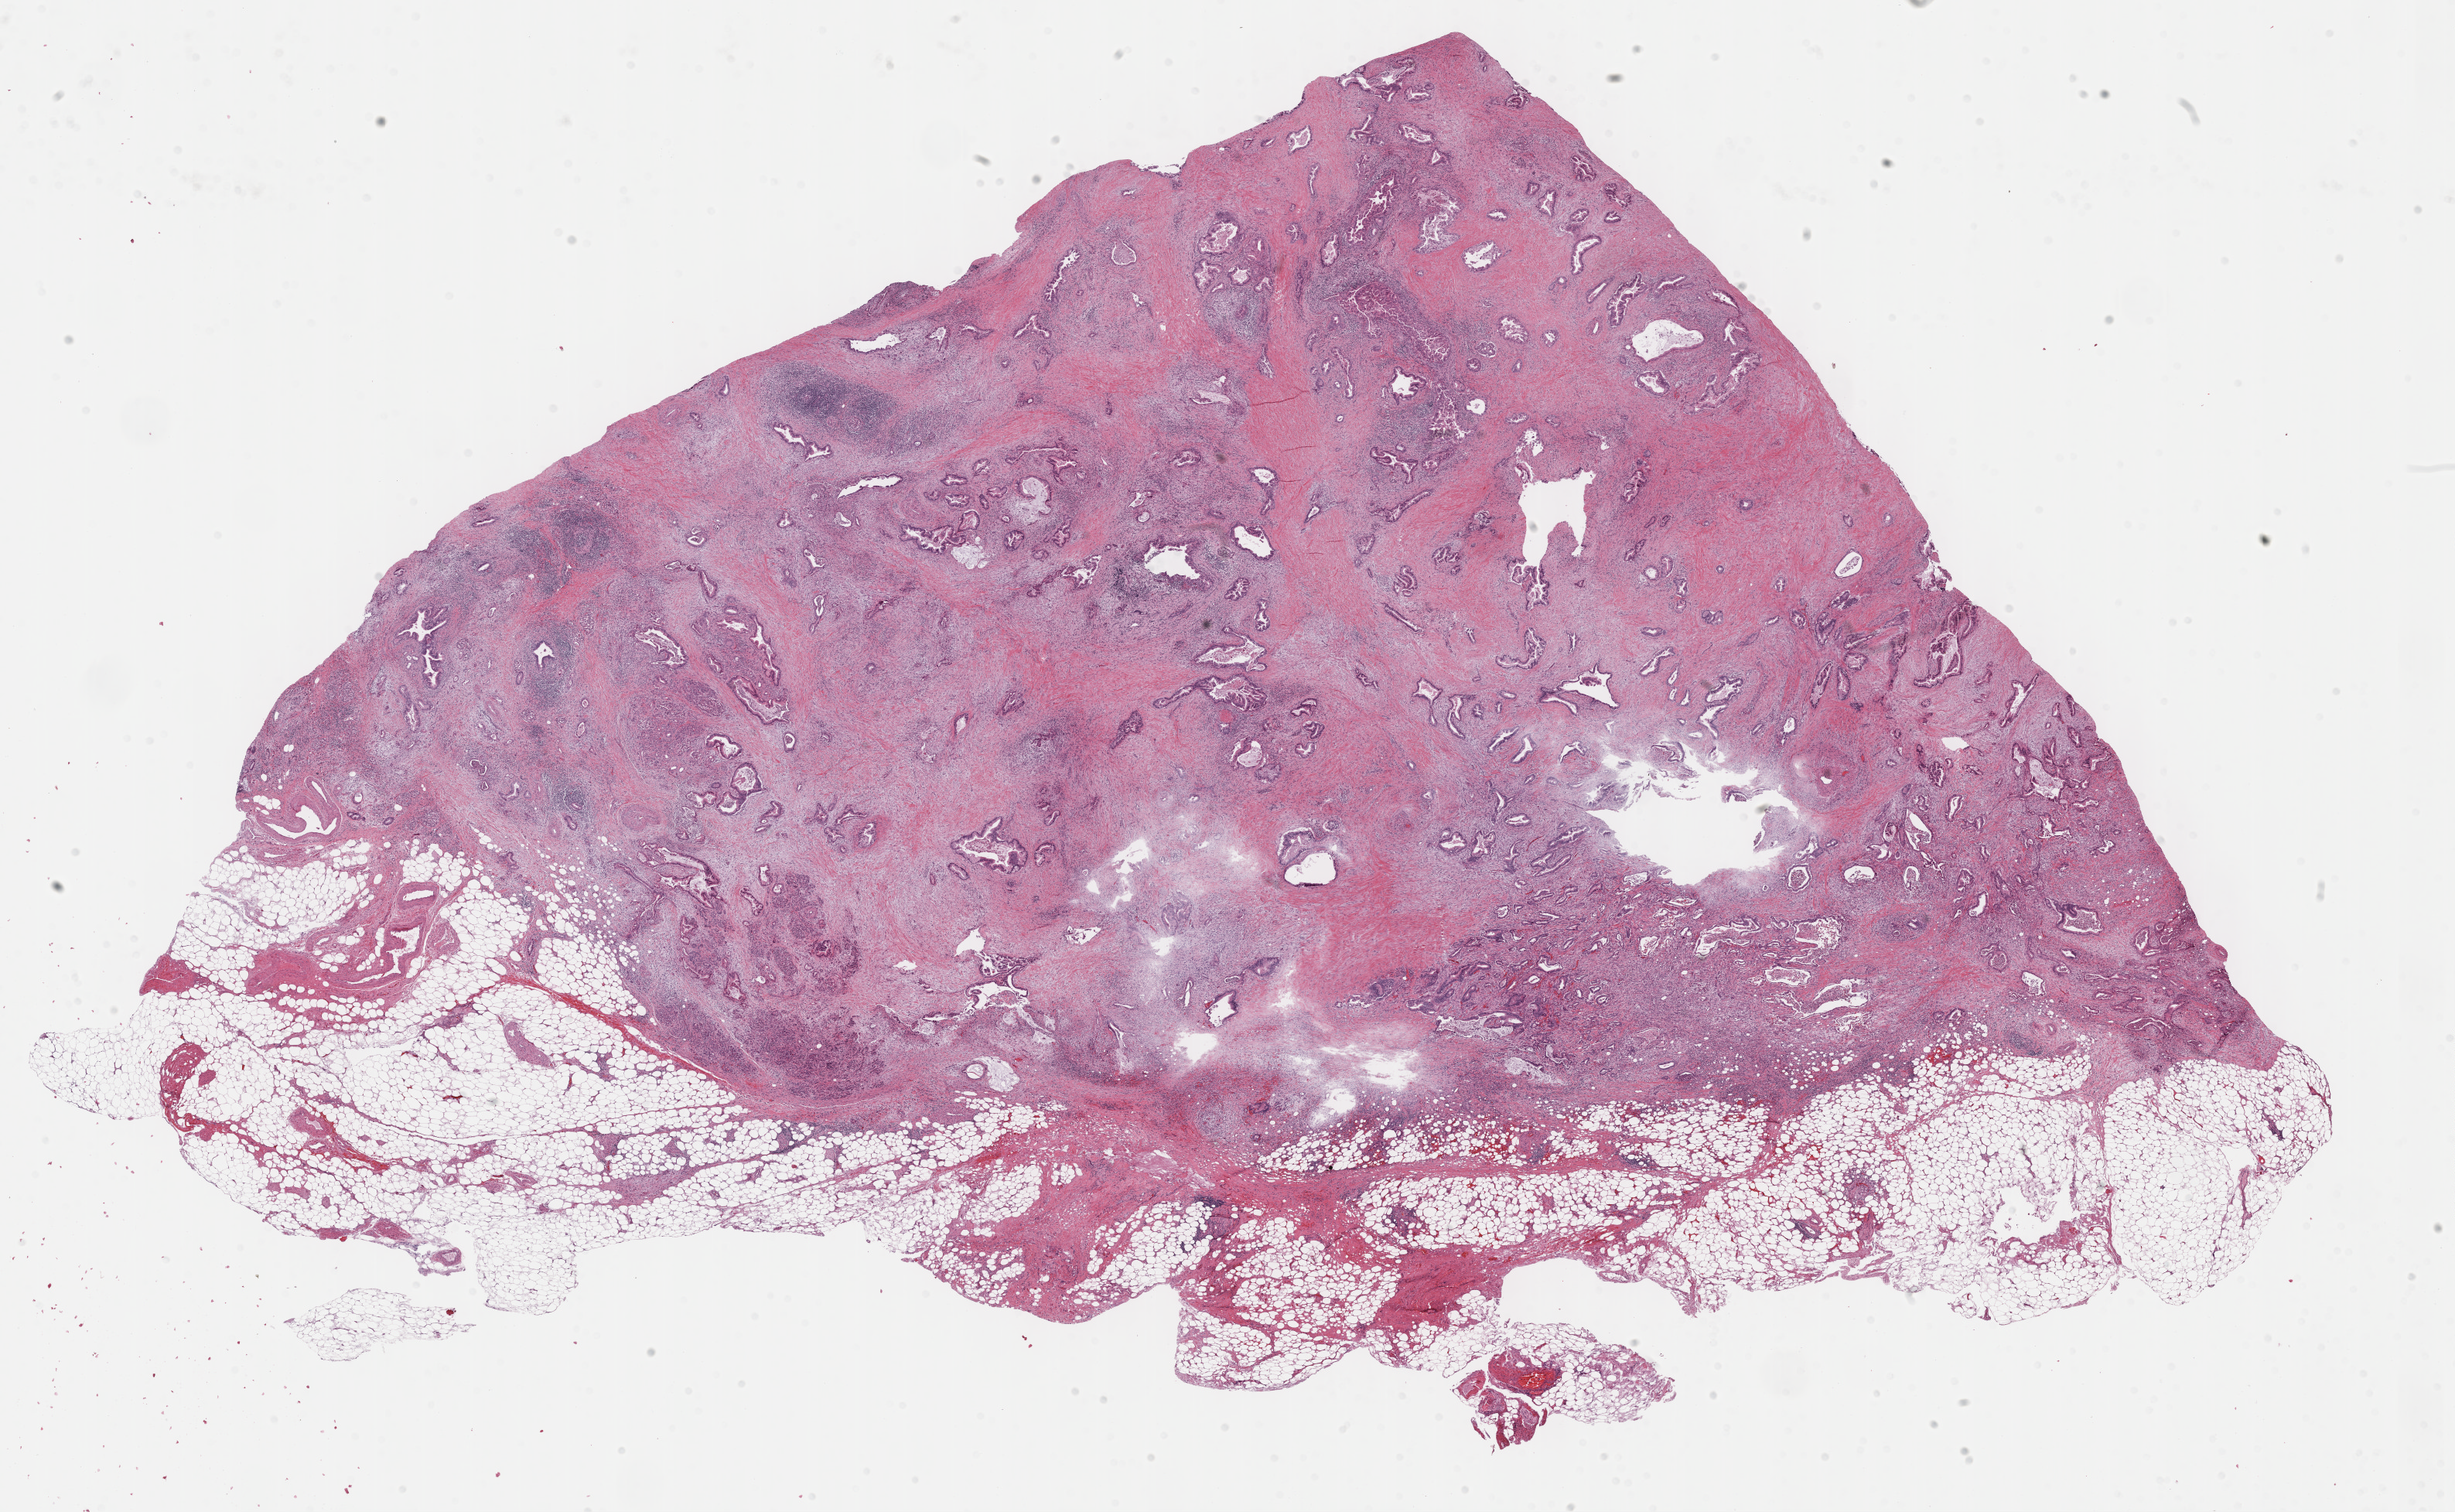
Hematoxylin and eosin (H&E) stained whole-slide image, whole scanned area (about 25.7 x 15.8 mm) shown as a low-resolution overview, formalin-fixed paraffin-embedded (FFPE) diagnostic section, sample: primary tumour, pancreas. Male patient; age at initial diagnosis 71 years. Histologic grade: G3 (poorly differentiated).
Histologic diagnosis: Infiltrating duct carcinoma, NOS (head of pancreas). Lymph nodes positive (case pathology): 3 of 27 examined. TNM: T3 N1 M0. AJCC pathologic stage: IIB.